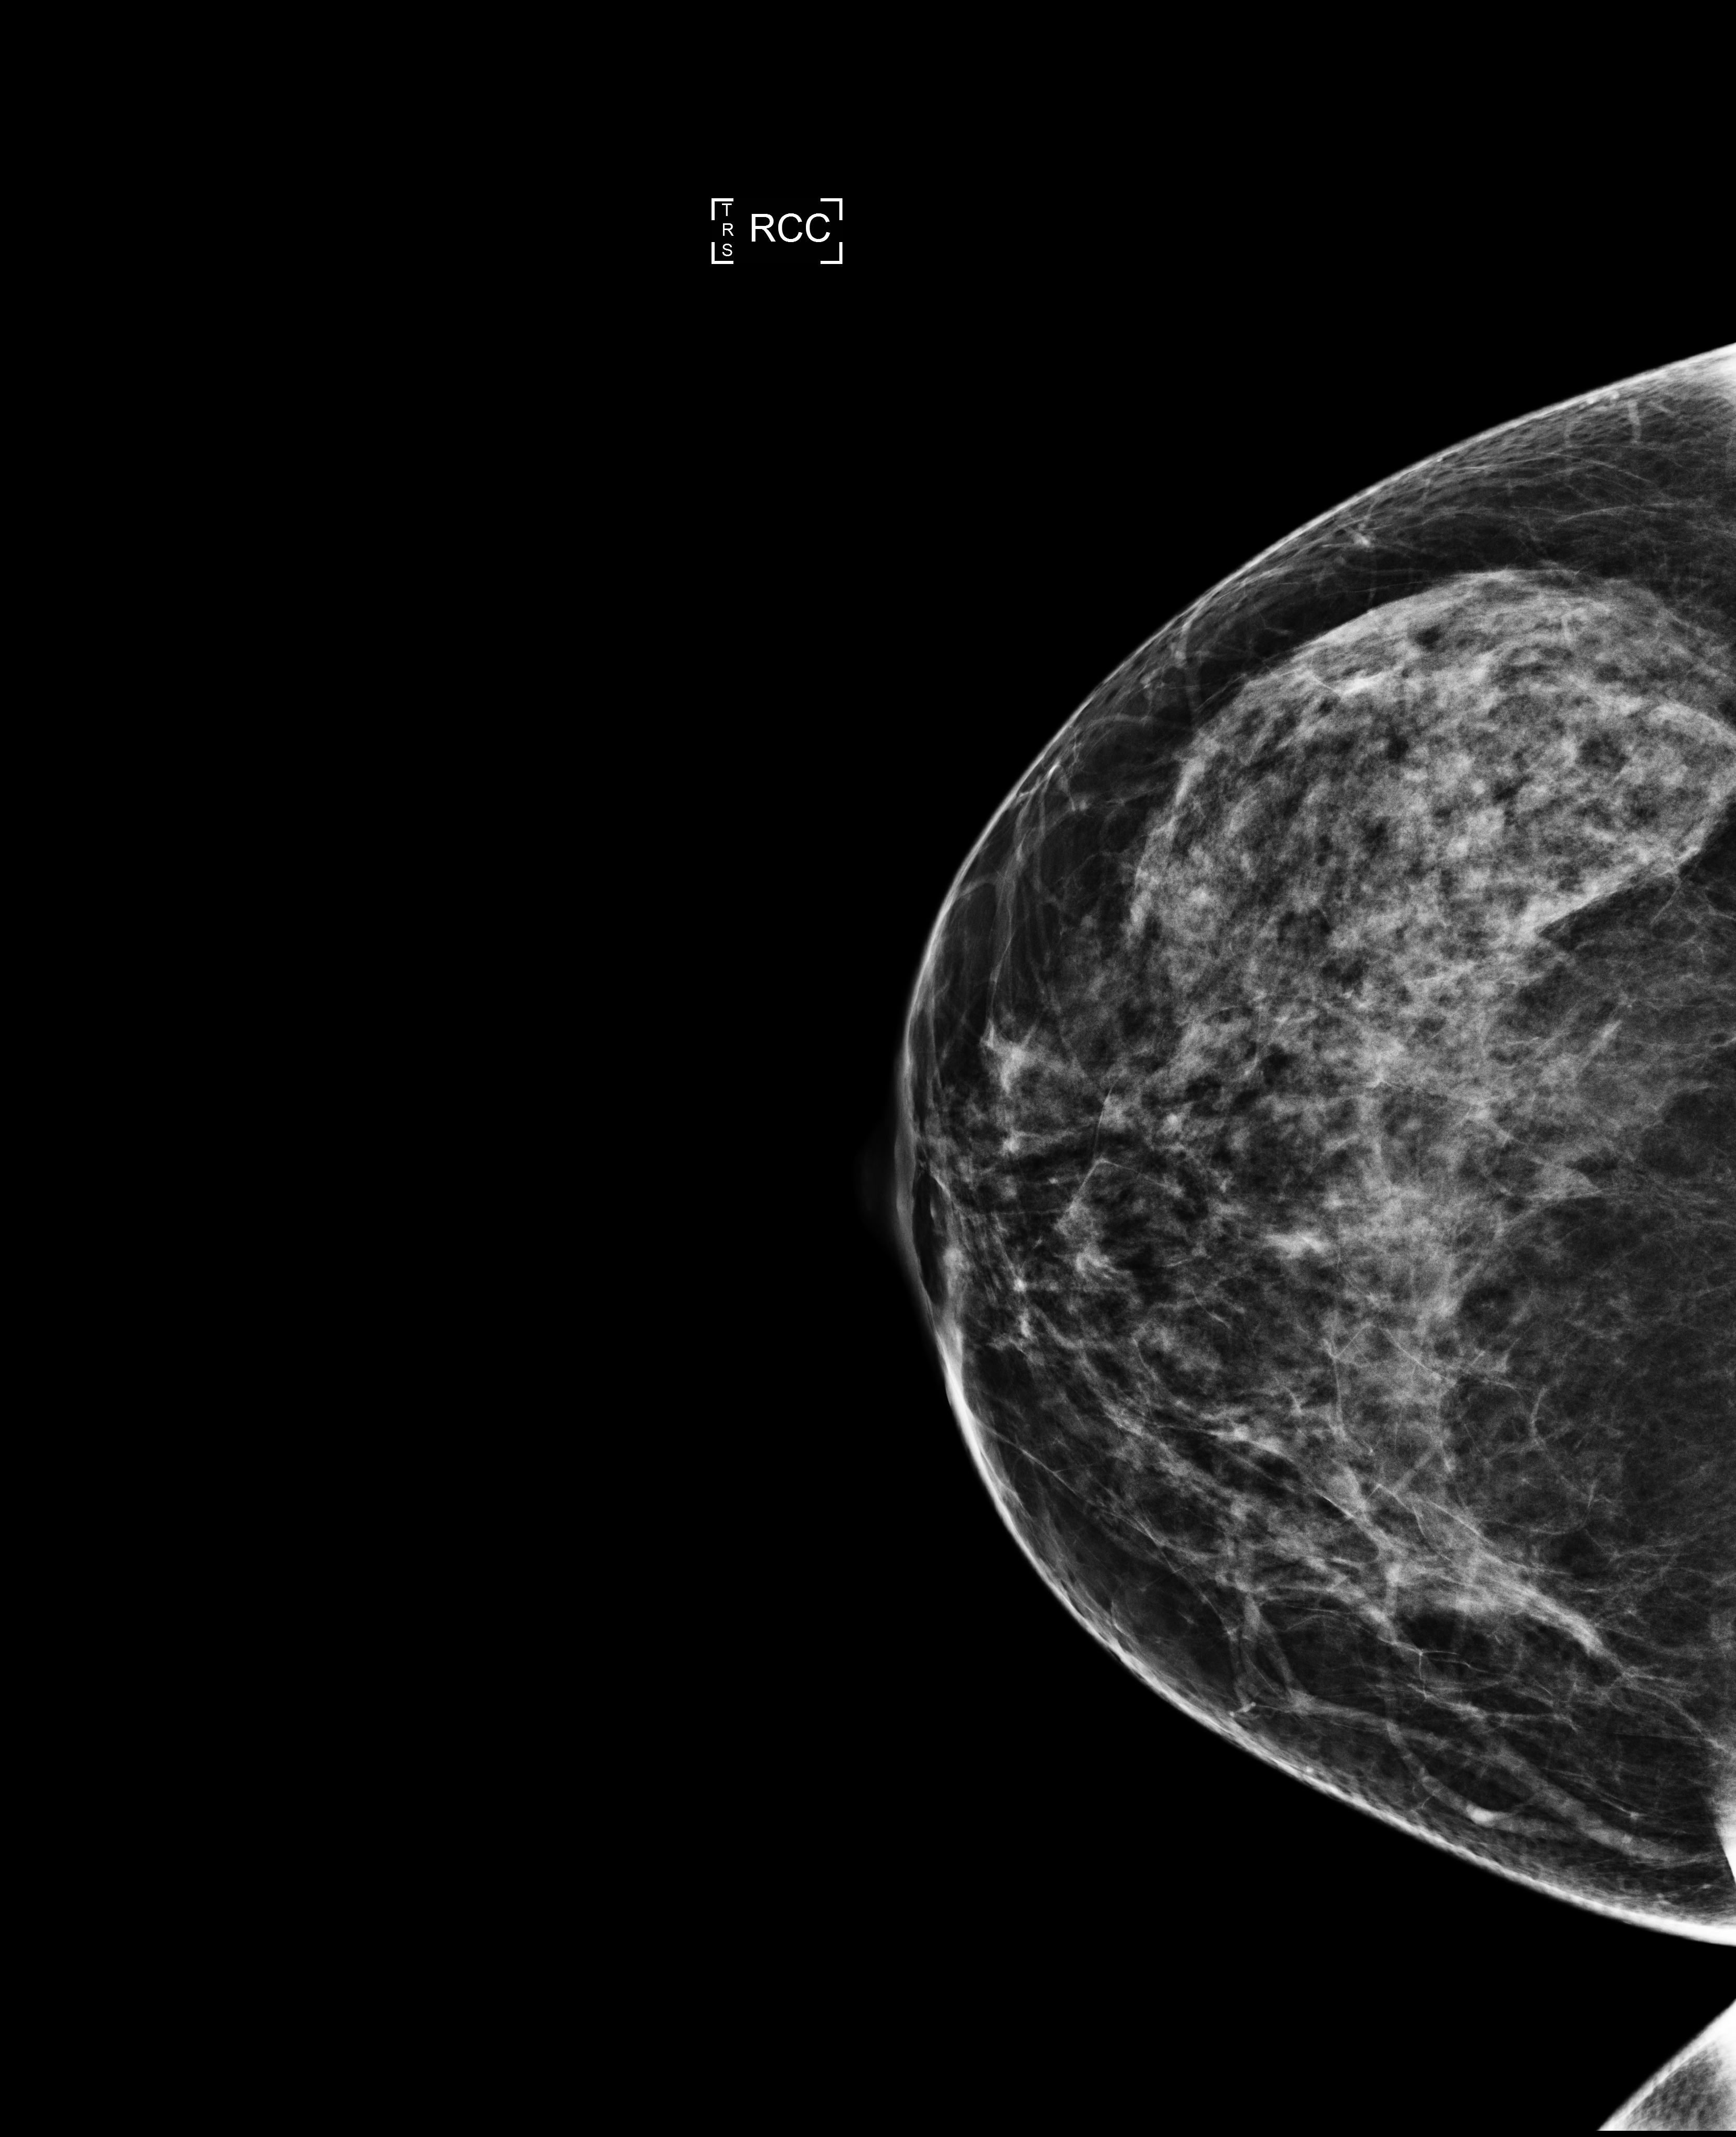
Digital mammogram (FFDM), right breast, cranio-caudal projection, annual screening mammography examination, system: Selenia Dimensions. Patient aged 44 years (female).
Breast density at the screening exam (both breasts): heterogeneously dense (BI-RADS density category c). Final BI-RADS assessment for this screening round (tomosynthesis exam, both breasts): category 2. Recall: no recall after this screen.